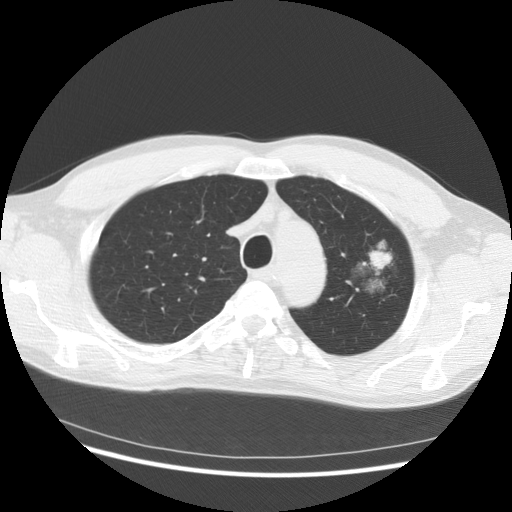
Low-dose screening chest CT, one axial slice; position 111 of 145 along the scan axis; 140 kVp; lung window (W 1500 / L -600 HU); 2.5 mm slice thickness; 512 × 512 image matrix, field of view 370 × 370 mm.
Annotated regions visible in this slice (expert manual segmentation):
- lesion 1 (tumor, upper lobe of left lung): bounding box (x1, y1, x2, y2) in pixels: (370, 242, 392, 269)